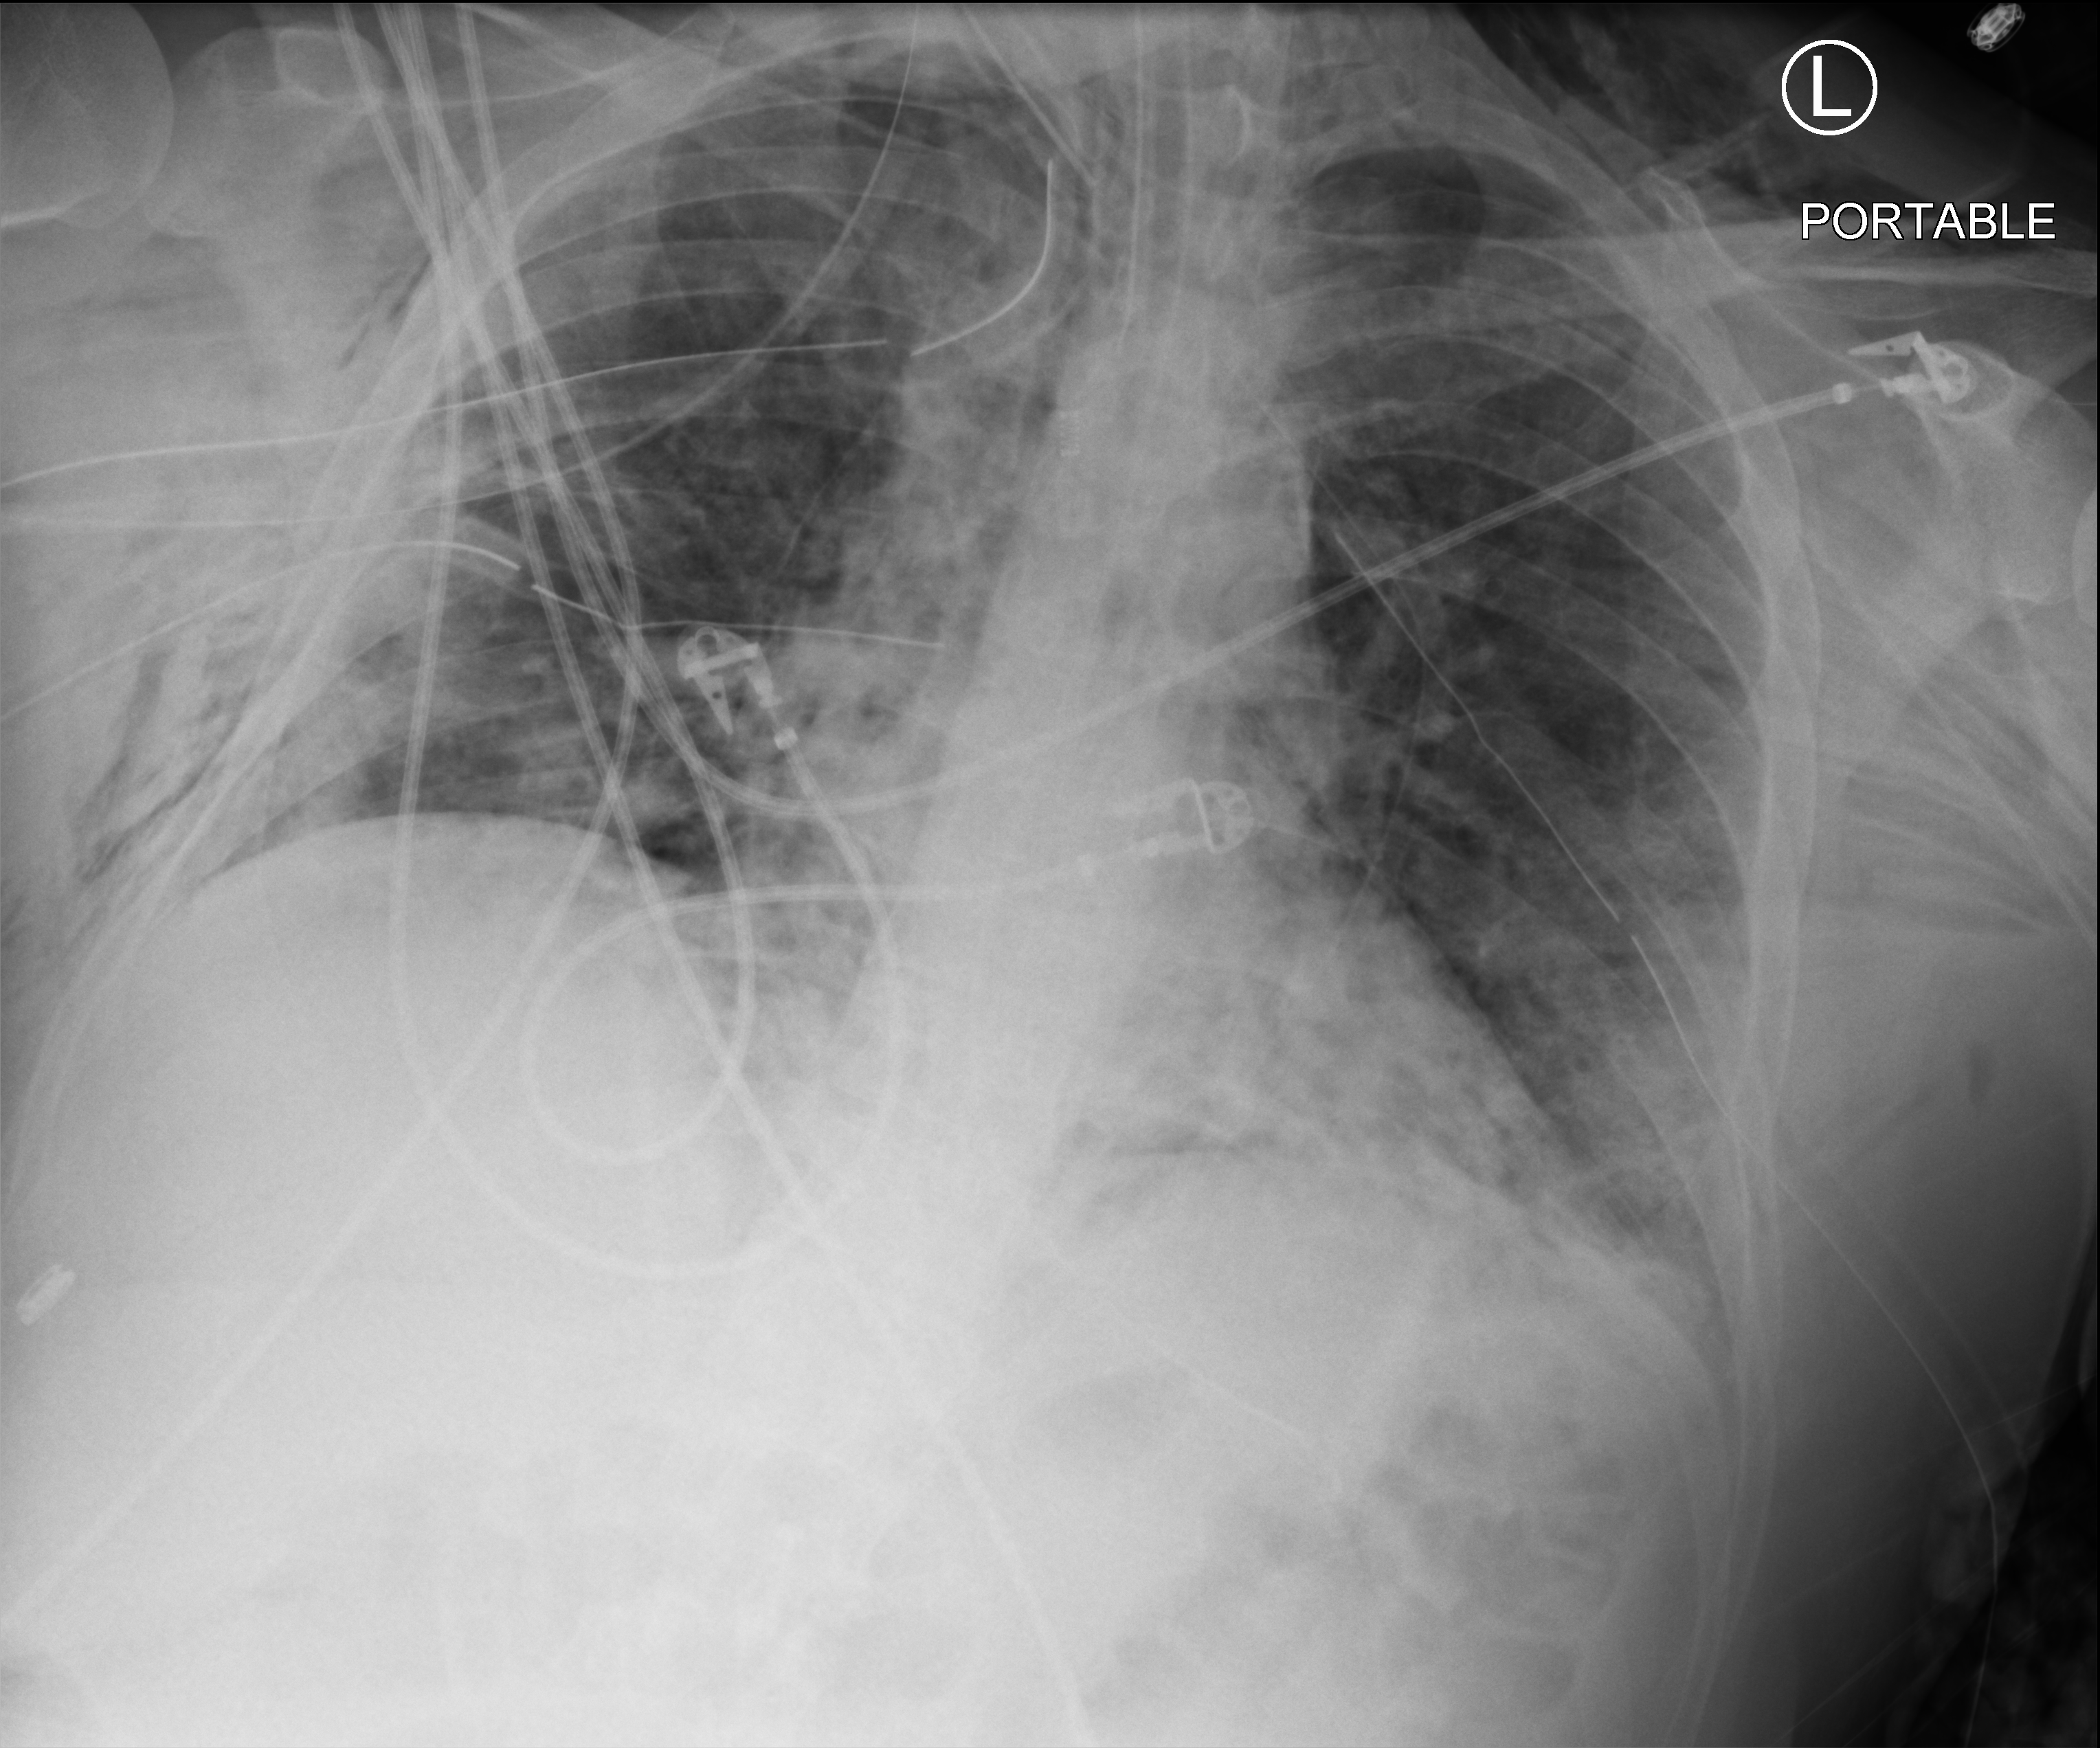
Chest X-ray (portable); anteroposterior (AP) projection. Male patient hospitalised with COVID-19, age 18–59 years.
From the hospital-stay record, not from the radiograph (when in the stay this image was taken is not recorded):
- mechanically ventilated during this hospital stay: yes
- hypertension (admission record): yes
- length of hospital stay: 63 days